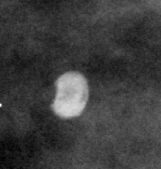
Cropped region of a digitized screen-film mammogram centred on a radiologist-marked abnormality; left breast; CC view.
- Finding: calcifications, morphology round and regular / eggshell; BI-RADS assessment category 2; benign; no additional work-up was recommended (benign without callback).